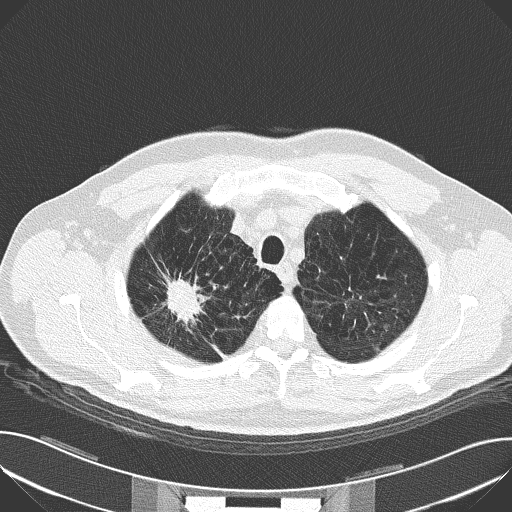
Chest CT (low-dose screening protocol), one axial image; baseline screening round; lung window (W 1500 / L -600 HU); 2 mm slice thickness; lung (sharp) reconstruction kernel (B50f); slice 24 of 159 in the series. Male participant, aged 59 years at enrolment. Current smoker at enrolment.
• Expert-annotated lung lesion, bounding box (x1, y1, x2, y2) in pixels: (154, 260, 218, 328).
• The screening reader recorded 4 non-calcified nodules or masses ≥4 mm on this exam; which of them this box marks is not recorded.
• Later outcome: lung cancer diagnosed 44 days after this screen — squamous cell carcinoma, NOS, right upper lobe, moderately differentiated (G2), stage IA (AJCC 6th edition), 30 mm at pathology.